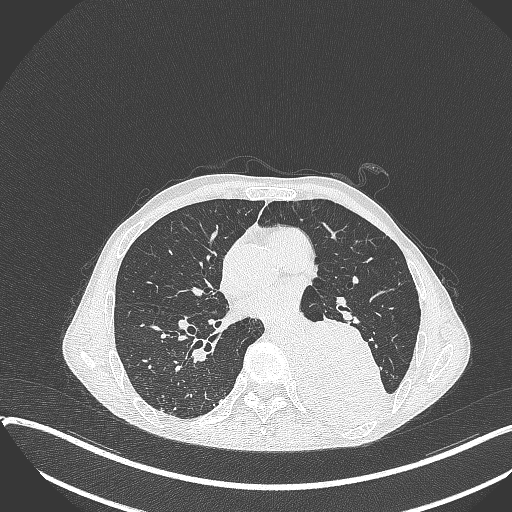
Chest CT, one axial slice; position 175 of 401 along the scan axis; reconstruction kernel B70f; lung window (W 1500 / L -600 HU); 1 mm slice thickness; 512 × 512 image matrix, field of view 400 × 400 mm. Patient: male, 57 years. From the clinical record (not read from this slice): clinical TNM (as recorded): T4 N0 M0.
Outlined on this slice (rectangle marked by the reading radiologist):
- lung tumour (recorded histology: squamous cell carcinoma): bounding box (x1, y1, x2, y2) in pixels: (294, 317, 386, 425)